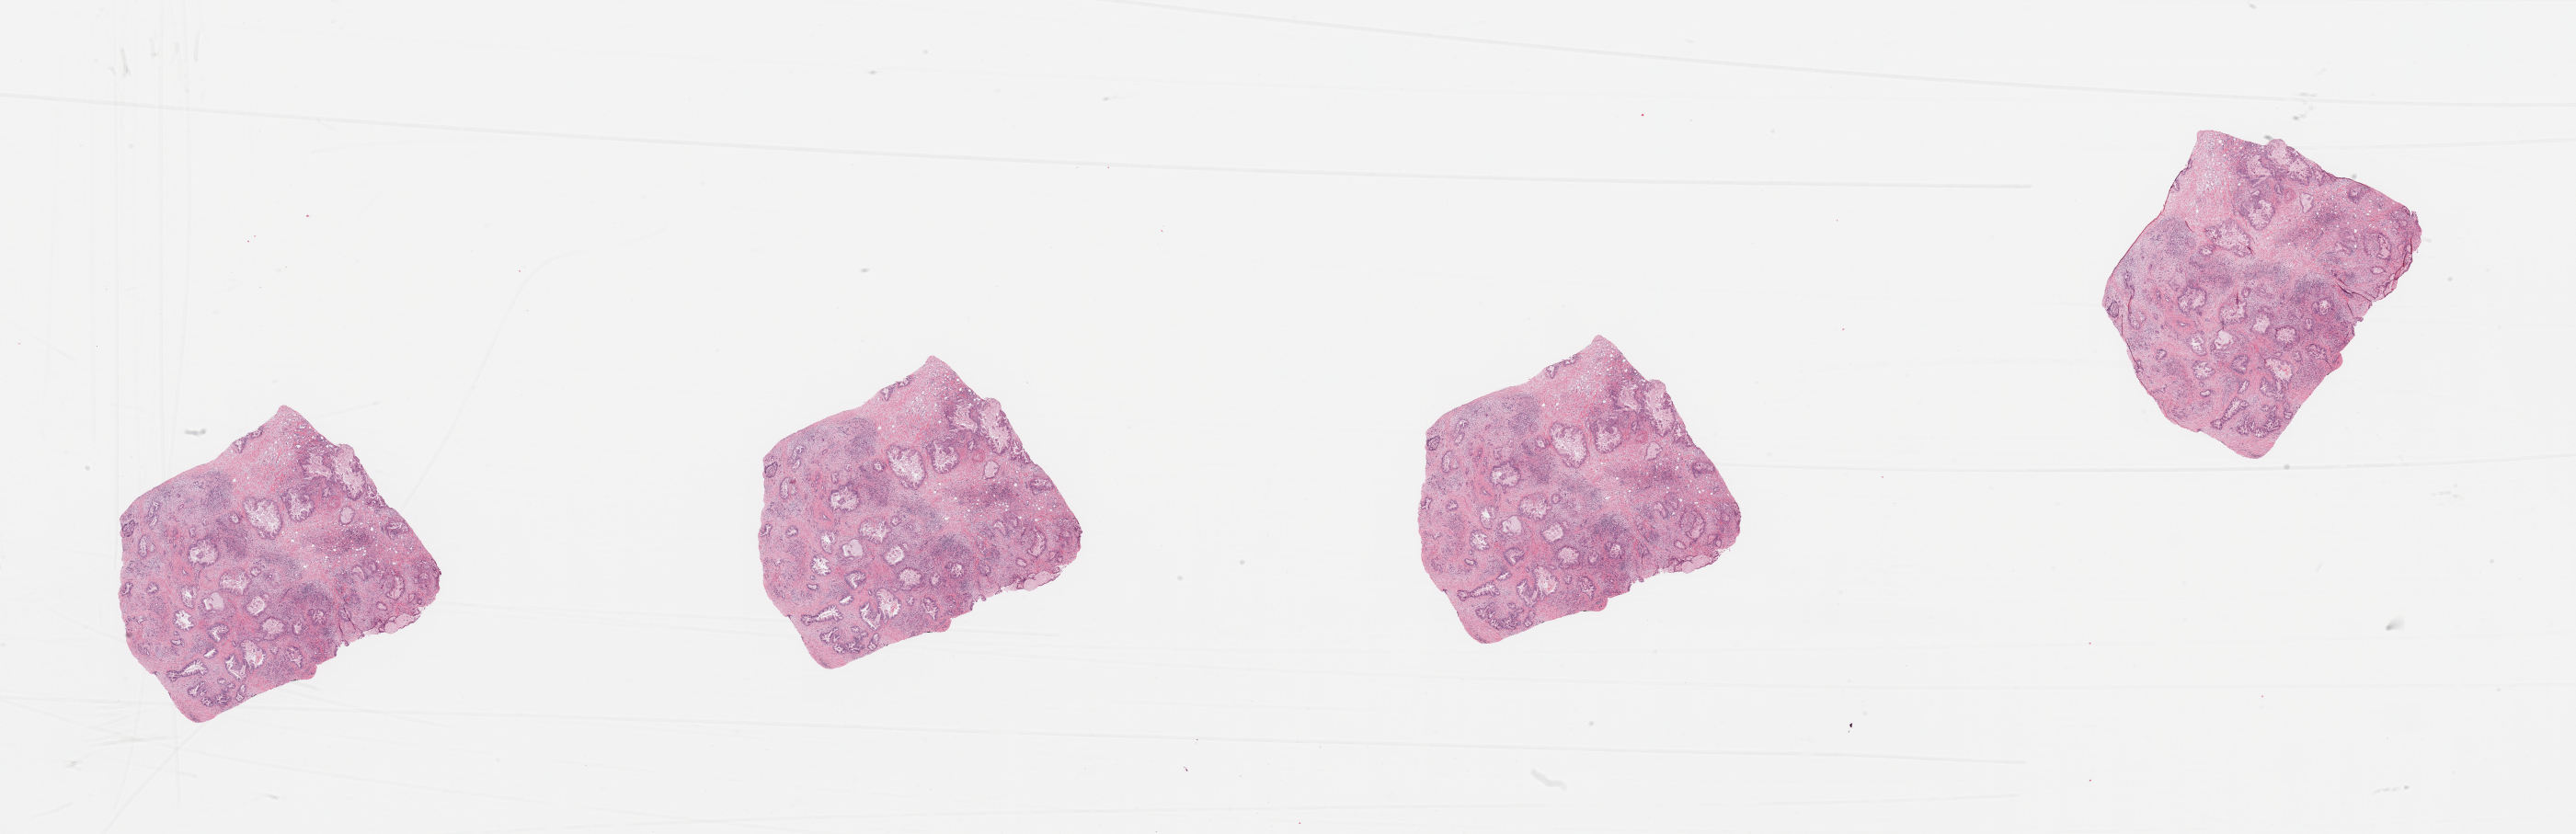
Digitized H&E-stained tissue section (whole slide) — low-resolution overview of the scanned area, about 44.3 x 14.3 mm. Tumour tissue sample, sampled site: pancreas. Male, 71 y/o. Histologic grade: G2 (moderately differentiated). Pathologist review of this section (percent, as recorded): tumour nuclei 40%, necrosis 0%.
AJCC pathologic stage: IIB. Primary tumour site (as recorded): head. Diagnosis: Infiltrating duct carcinoma, NOS.